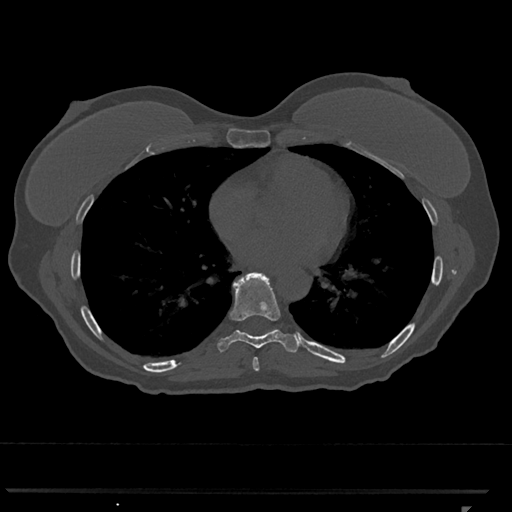
CT including the spine, one axial slice. Position 663 of 793 along the scan axis. Reconstruction kernel Br40s/3. 120 kVp. Bone window (W 1800 / L 400 HU). 0.5 mm slice thickness. 512 × 512 image matrix. Patient: female, 62 years. From the clinical record (not read from this slice): primary cancer: renal.
Structures marked on this image (semi-automatically segmented with operator editing):
- T7 vertebra: box from (x=252, y=357) to (x=260, y=371) px
- T8 vertebra: (x=218, y=272)–(x=301, y=353)